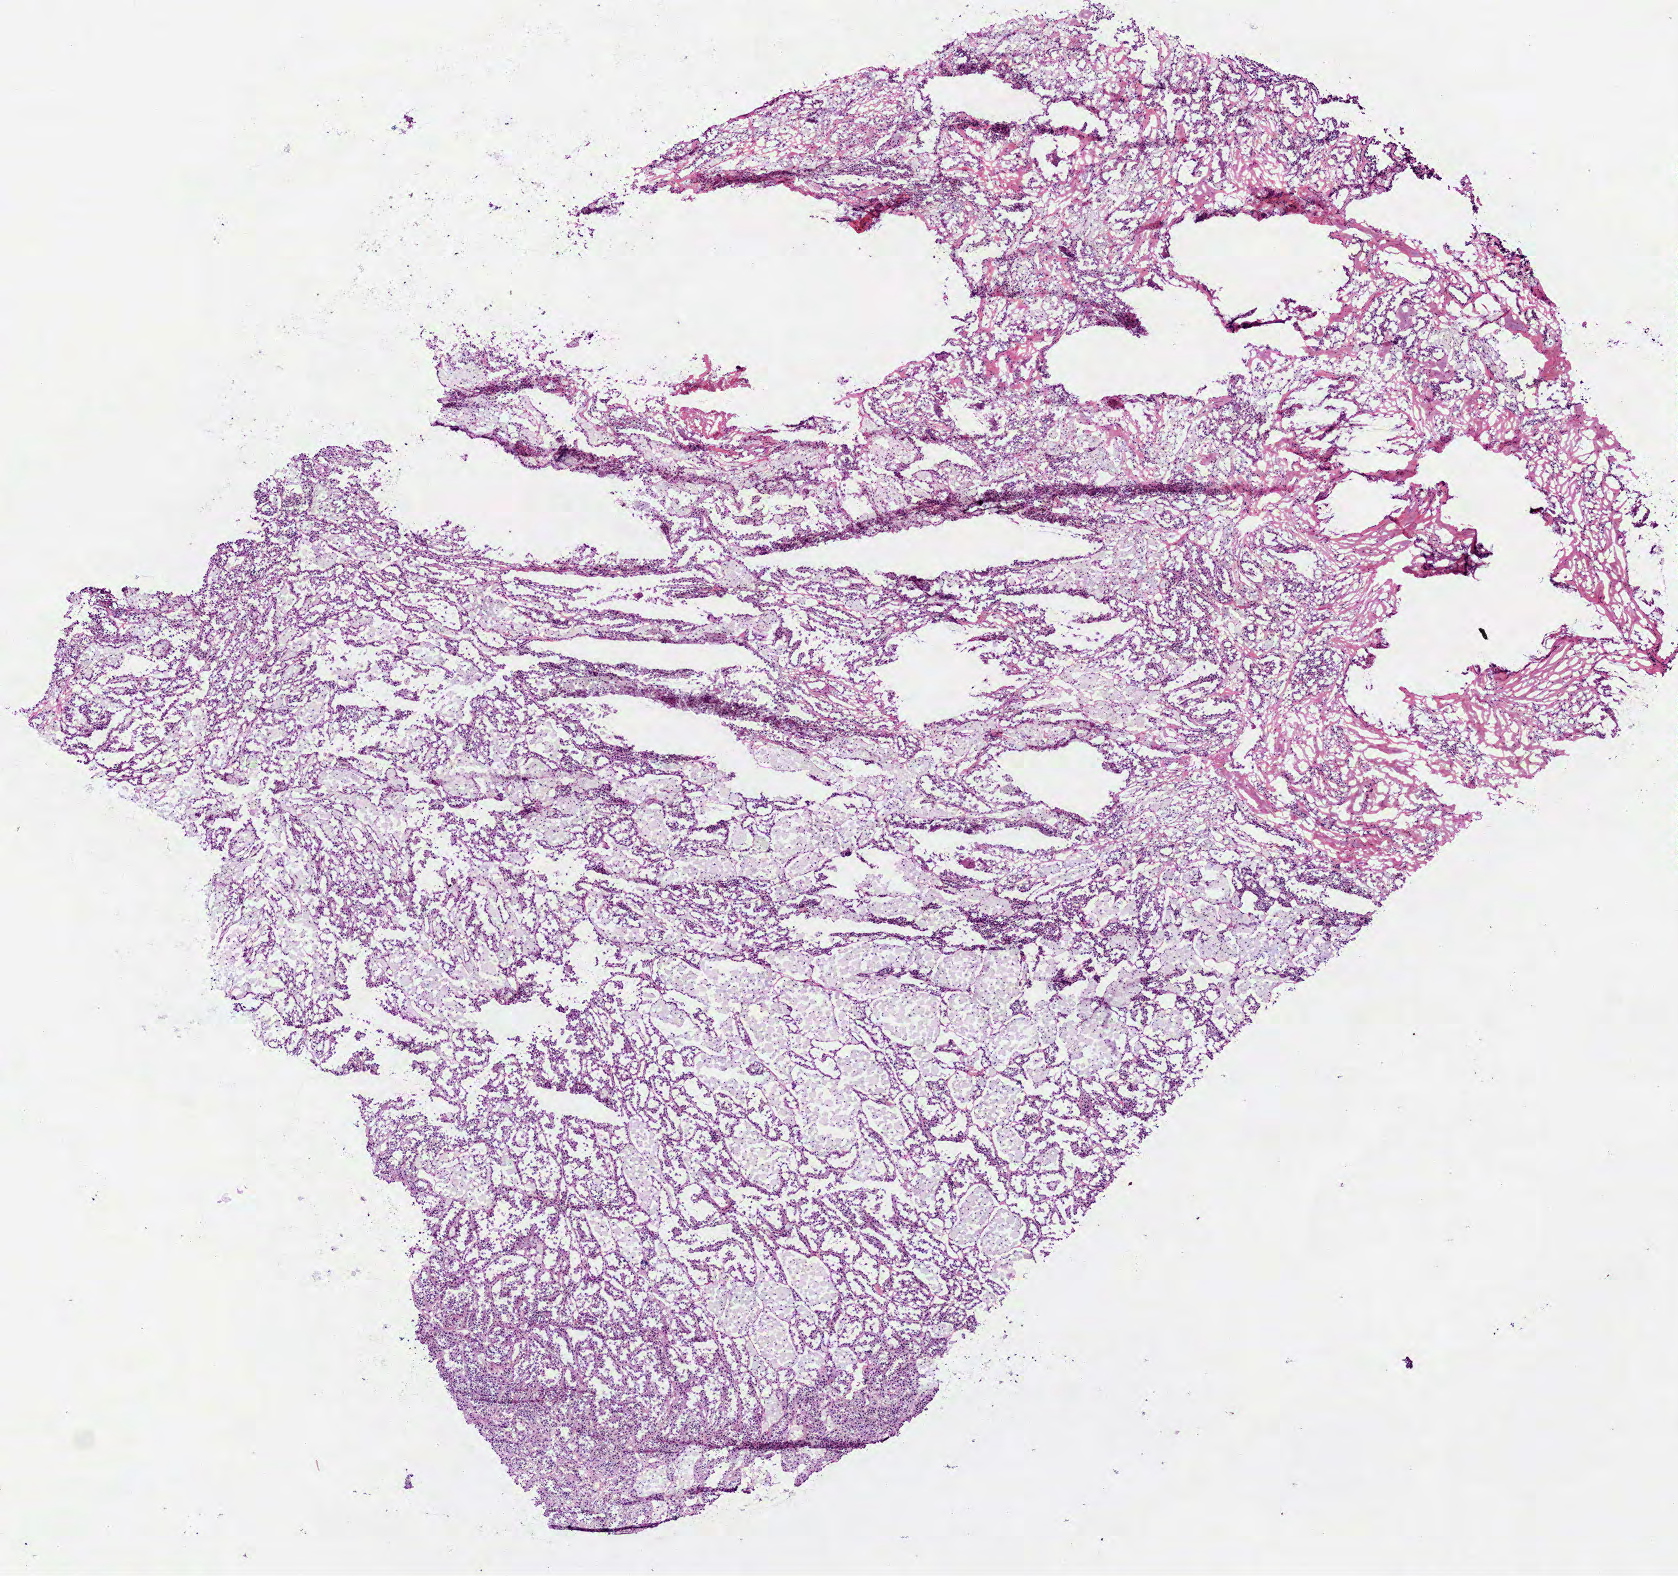
H&E-stained whole-slide image — low-resolution overview of the scanned area, about 6.8 x 6.4 mm, frozen section, sample: primary tumour, kidney. Male patient; age at initial diagnosis 83 years. Composition of this section per pathologist review: tumour cells 100%, tumour nuclei 75%, normal cells 0%, stromal cells 0%, necrosis 0%. Infiltration values recorded for this section: lymphocyte infiltration 0%, monocyte infiltration 20%, neutrophil infiltration 0%.
• laterality: left
• diagnosis: Papillary adenocarcinoma, NOS
• AJCC pathologic stage: I (7th edition)